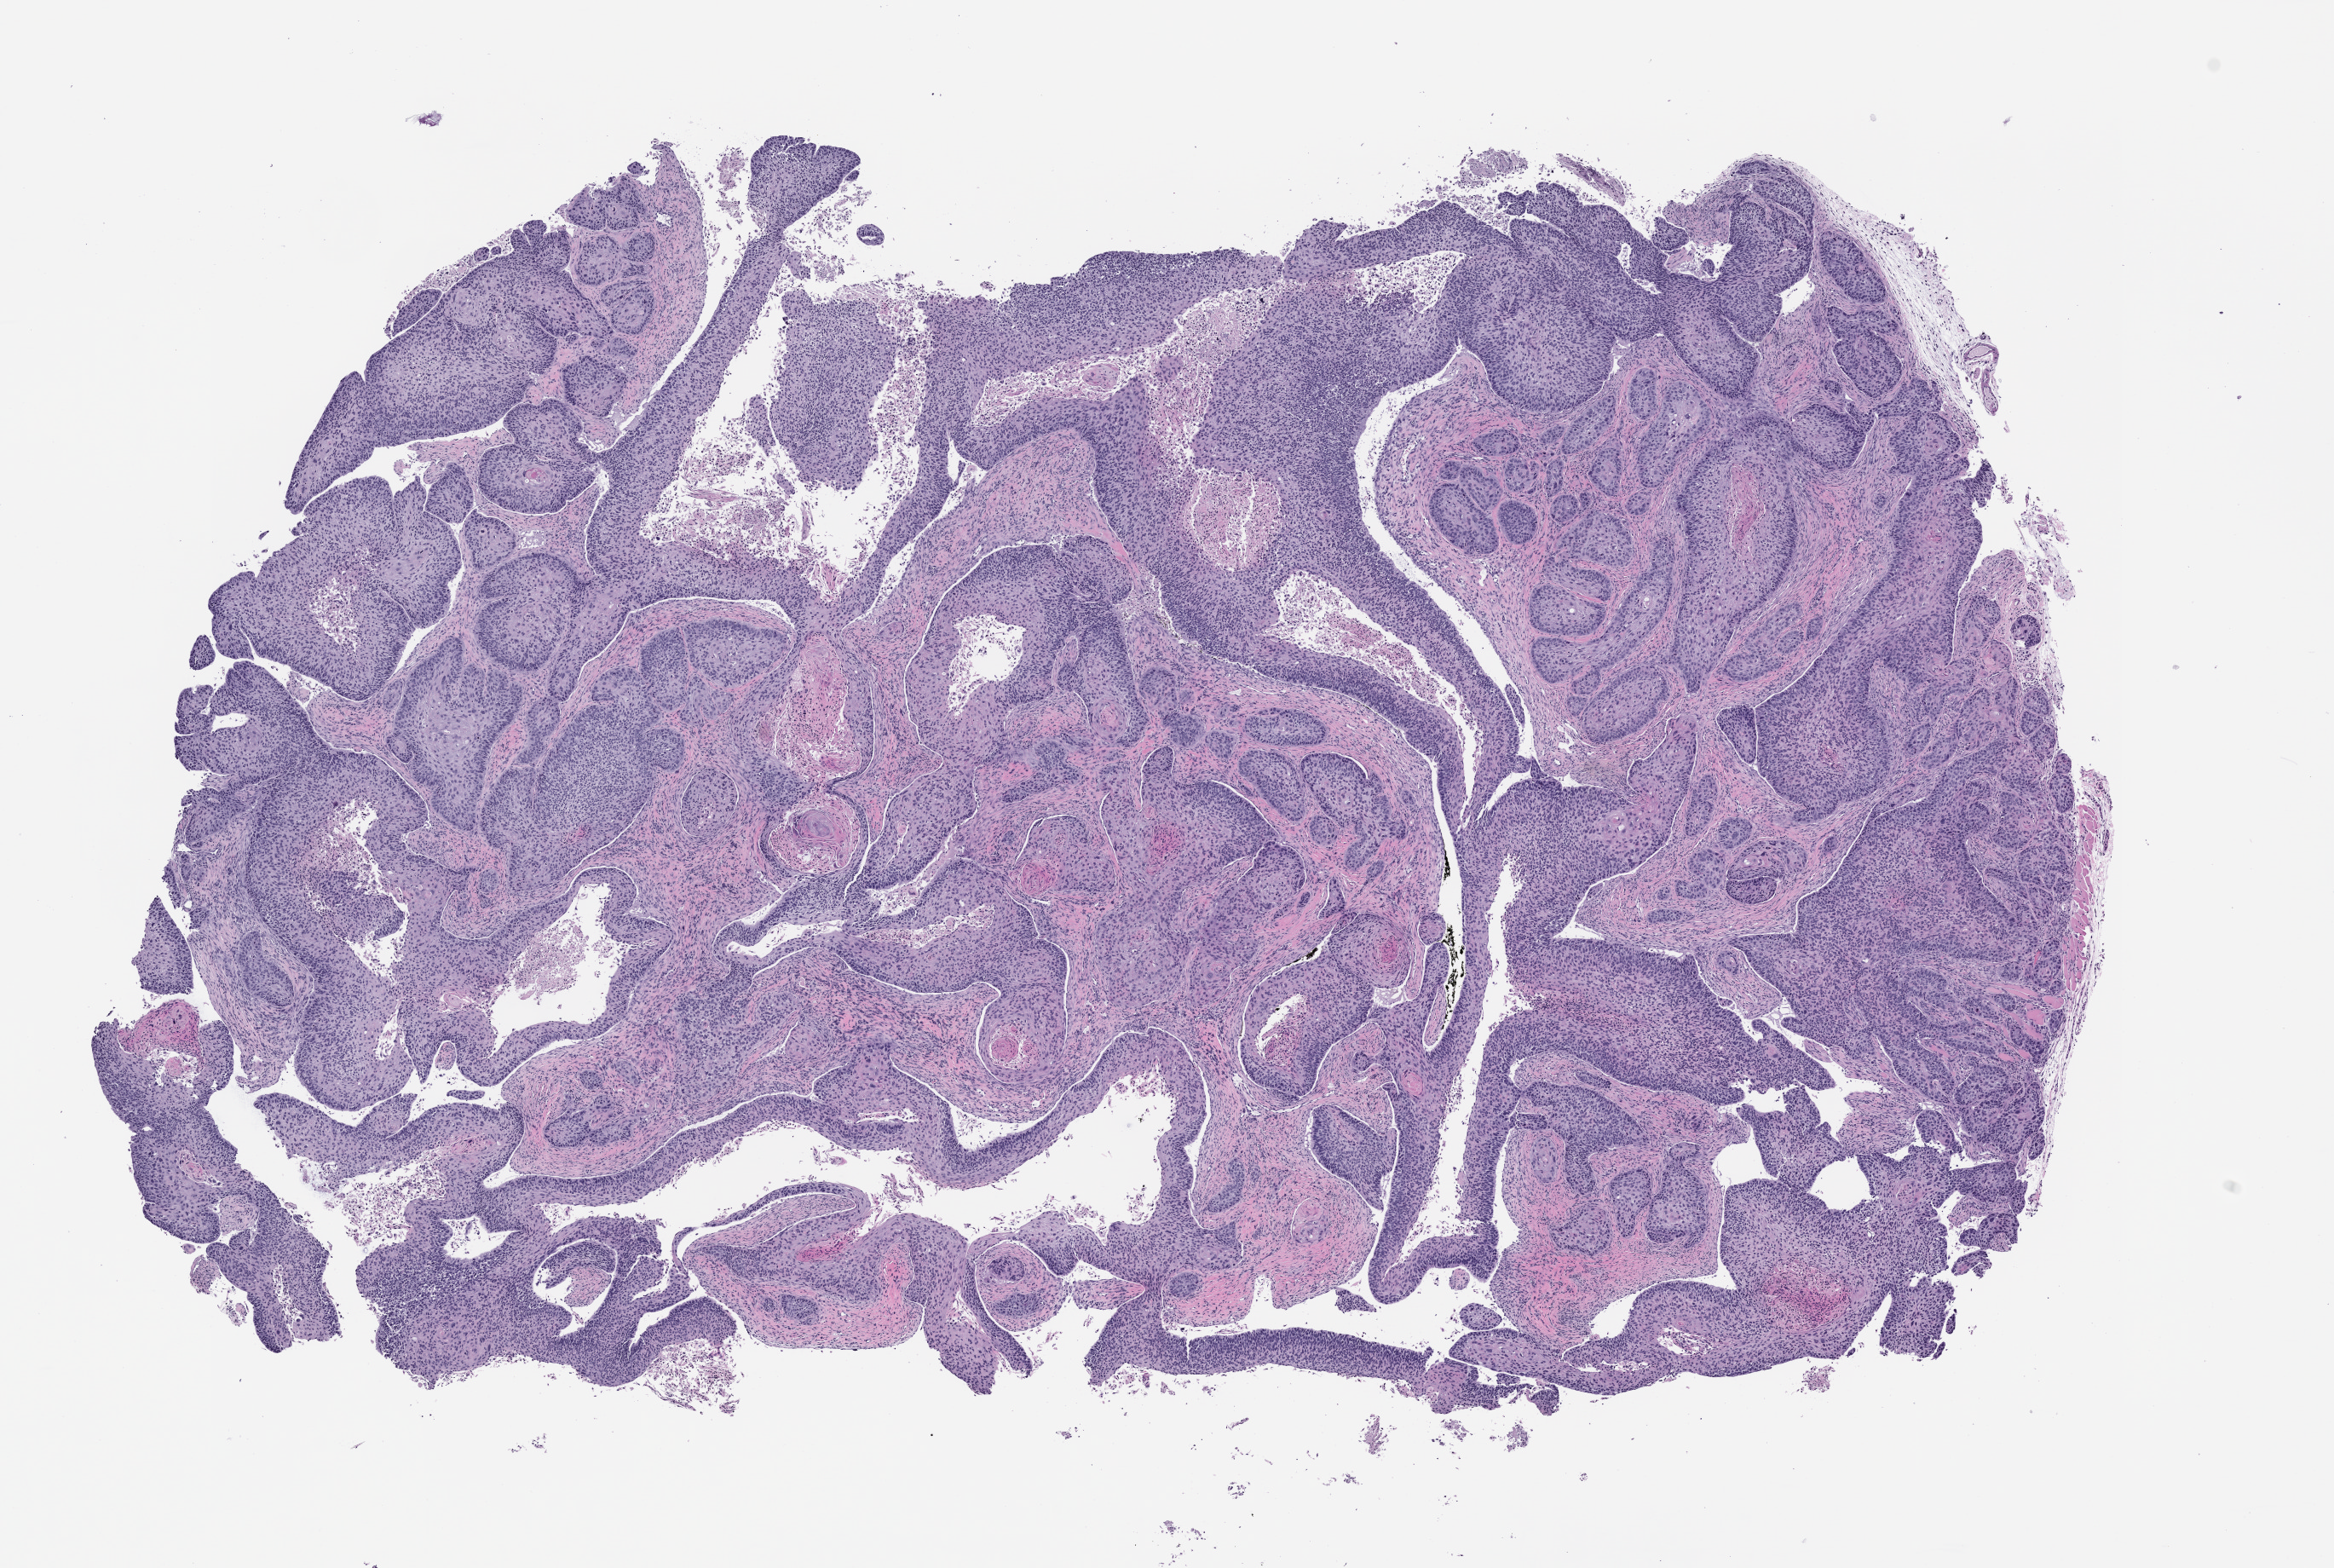
Whole-slide image, H&E: patient-derived xenograft (human tumor grown in a mouse), passage 3 — a low-resolution overview of the entire scanned area, about 11.0 x 7.4 mm; formalin-fixed paraffin-embedded section; tumor site category: head and neck.
• originating patient diagnosis: Head and Neck Squamous Cell Carcinoma